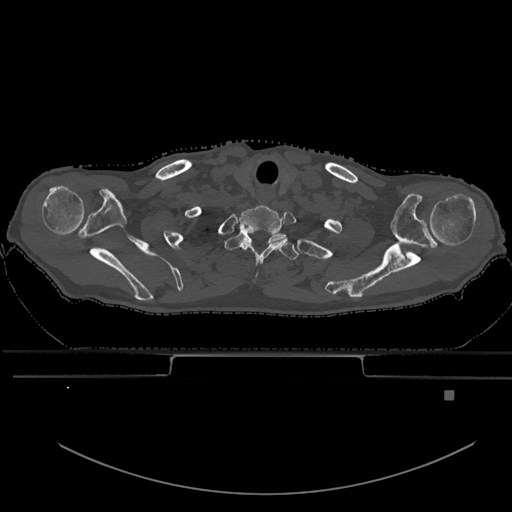
CT including the spine, one axial slice; slice 553 of 969 in the series (ordered by position); bone window (W 1800 / L 400 HU); 512 × 512 image matrix. Male patient, age 82 years. Case-level facts recorded for this patient, not image findings: primary cancer: prostate; vertebrae with lytic lesions (as recorded): T11, T9, T8, T2.
Outlined on this slice (semi-automatic segmentation, software-assisted and operator-edited):
- T1 vertebra: box from (x=225, y=231) to (x=299, y=260) px